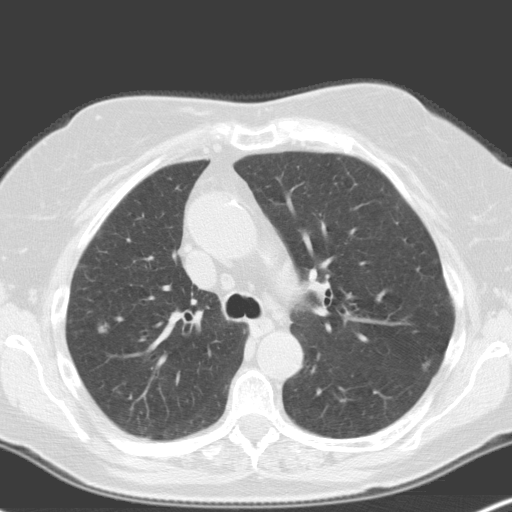
Low-dose screening chest CT, one axial slice; position 116 of 160 along the scan axis; 120 kVp; lung window (W 1500 / L -600 HU); 512 × 512 image matrix.
Structures marked on this image (manually delineated by an expert):
- lesion 3 (nodule): bounding box [x1, y1, x2, y2] px = [97, 326, 107, 333]